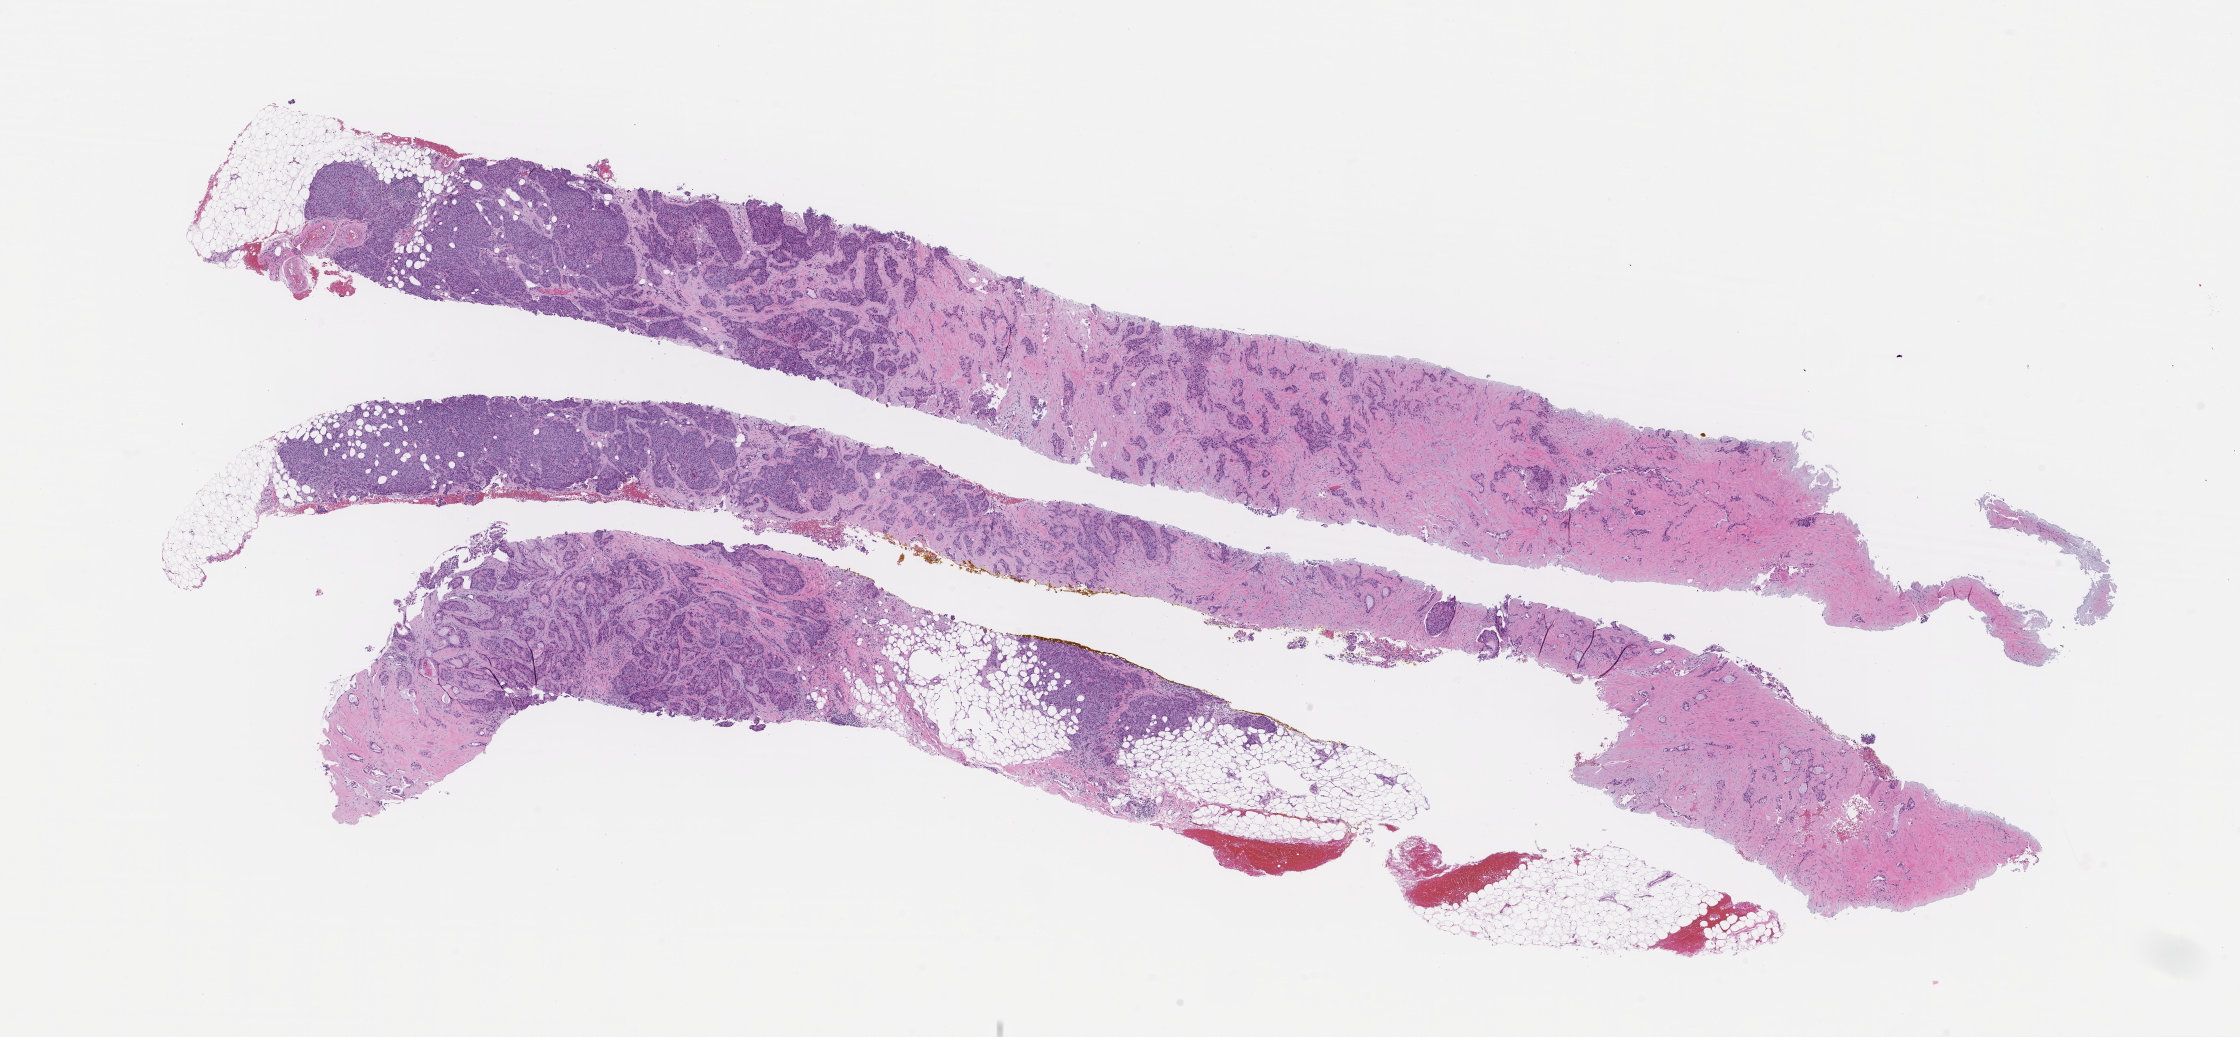
Digitized haematoxylin and eosin-stained section — shown as a low-resolution overview of the whole scanned area (about 18.1 x 8.4 mm); FFPE section; site: breast. Female patient.
- this section: primary tumor
- diagnosis: Invasive Breast Carcinoma